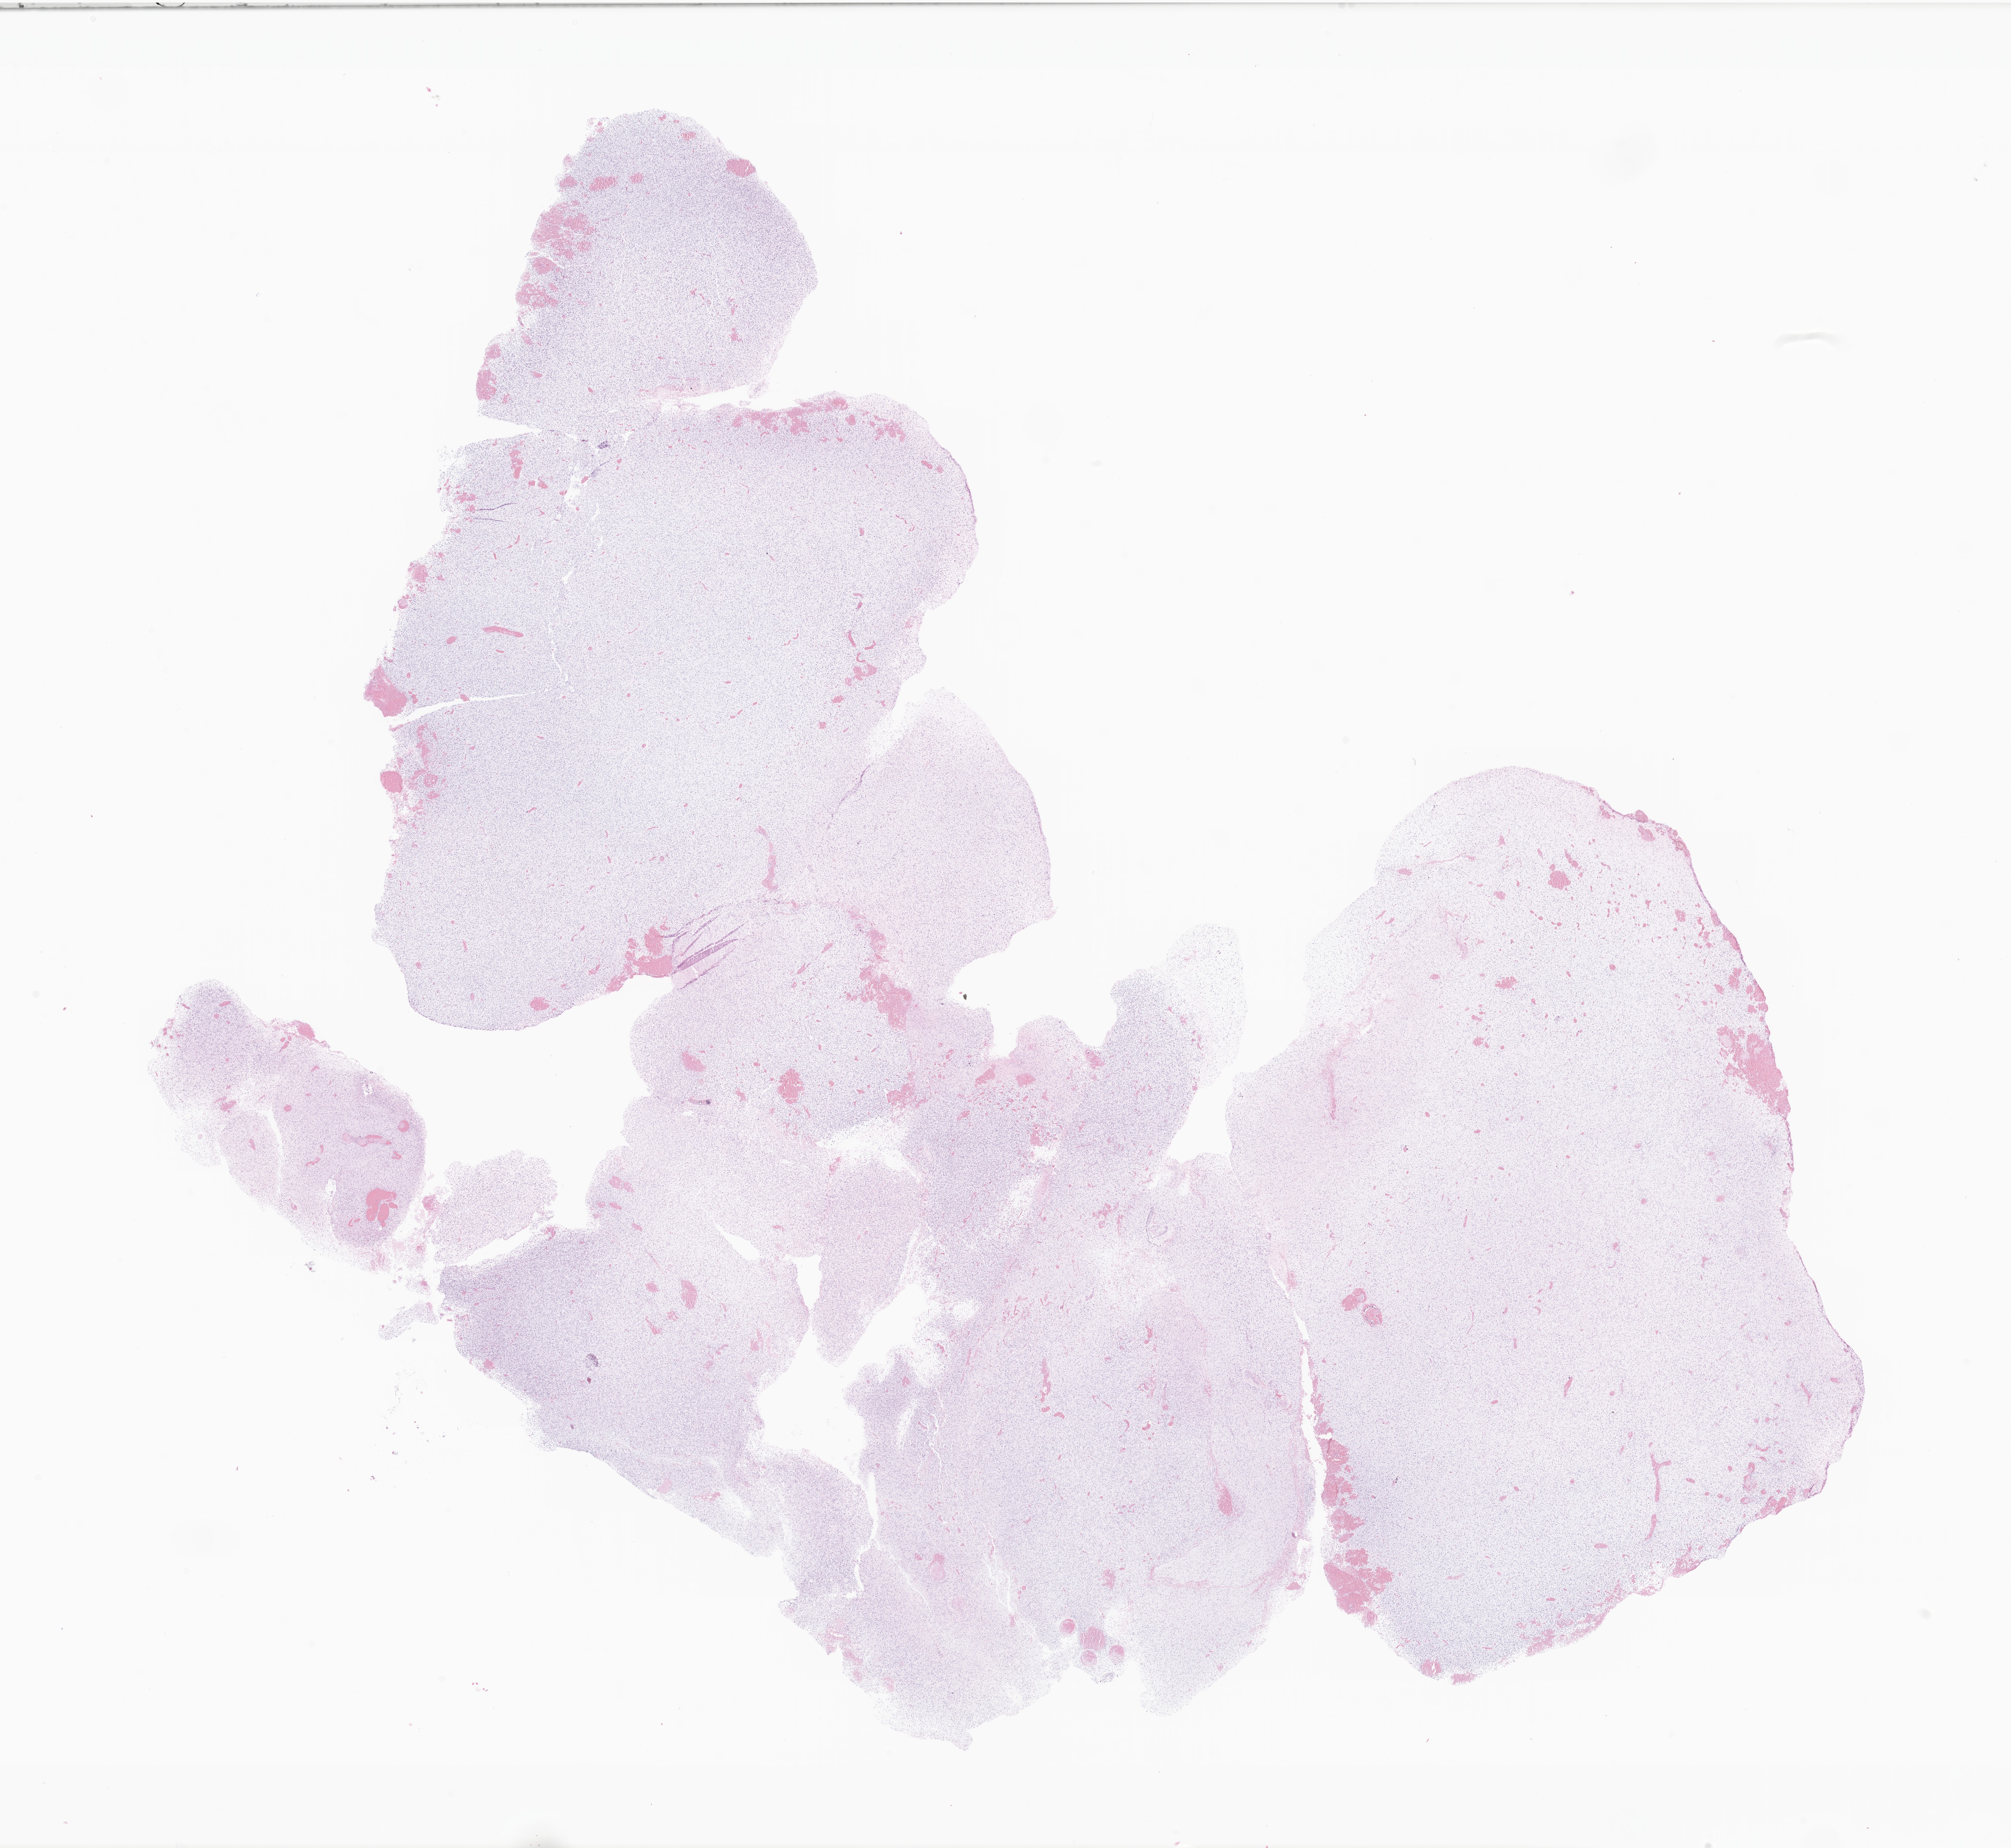
Digitized haematoxylin and eosin-stained section of tumor tissue from the temporal lobe — low-resolution overview of the scanned area, about 25.3 x 23.2 mm, FFPE section. Patient: female, age 94 months (7 years 10 months).
Diagnosis: Neoplasm, malignant.